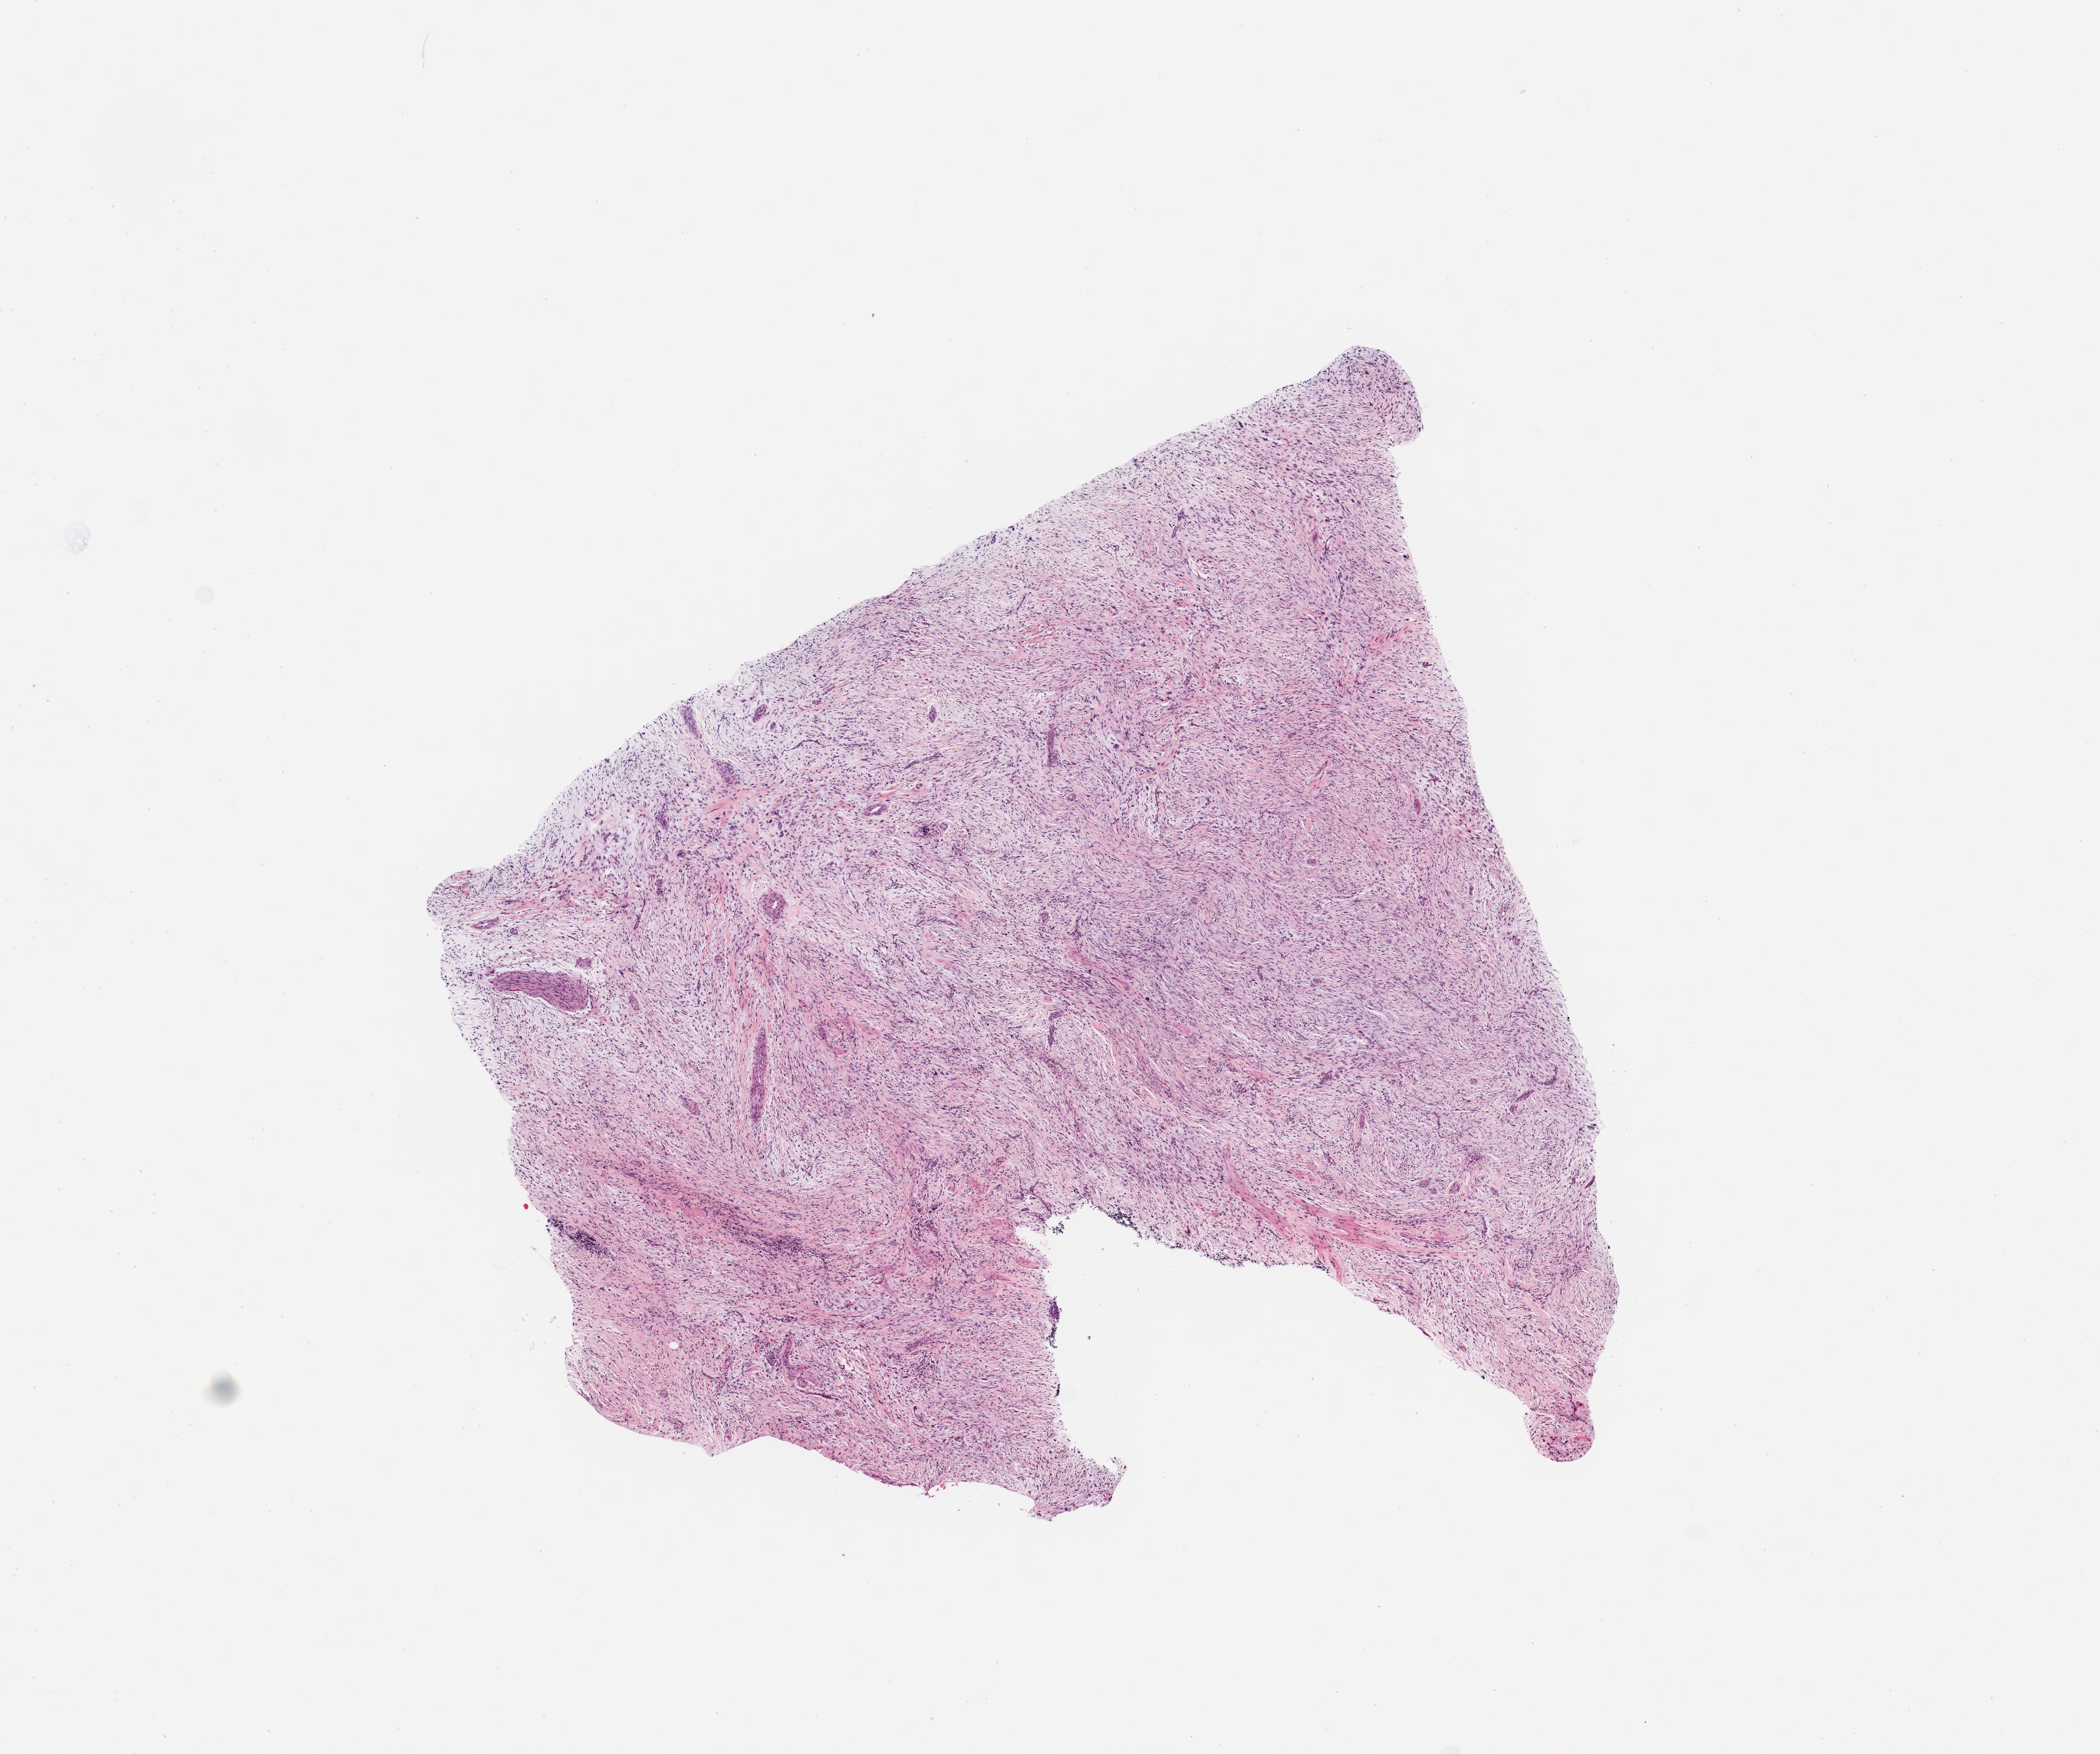
H&E whole-slide image, whole scanned area (about 10.8 x 9.0 mm) shown as a low-resolution overview, tumour tissue sample. Patient: male, age 65 years.
- primary tumour site (as recorded): retroperitoneum
- patient diagnosis (cohort enrolment): sarcoma (site not recorded at cohort level)